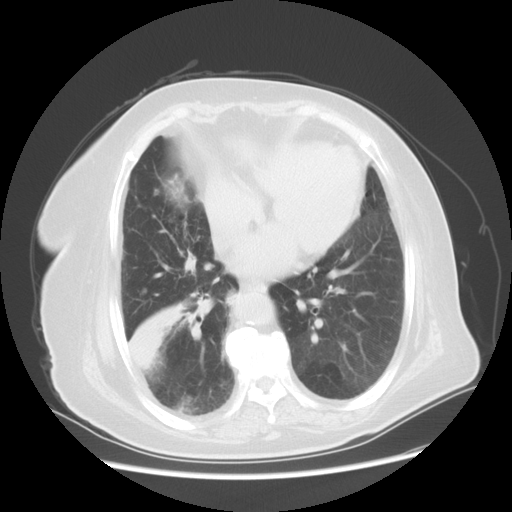
Chest CT, one axial slice. Position 22 of 56 along the scan axis. Reconstruction kernel STANDARD. 120 kVp. Lung window (W 1500 / L -600 HU). 512 × 512 image matrix, field of view 378 × 378 mm. Patient: female, 73 years. Case-level facts recorded for this patient, not image findings: clinical TNM (as recorded): T3 N0 M0.
Structures marked on this image (rectangle marked by the reading radiologist):
- lung tumour (recorded histology: adenocarcinoma): box from (x=123, y=295) to (x=189, y=383) px